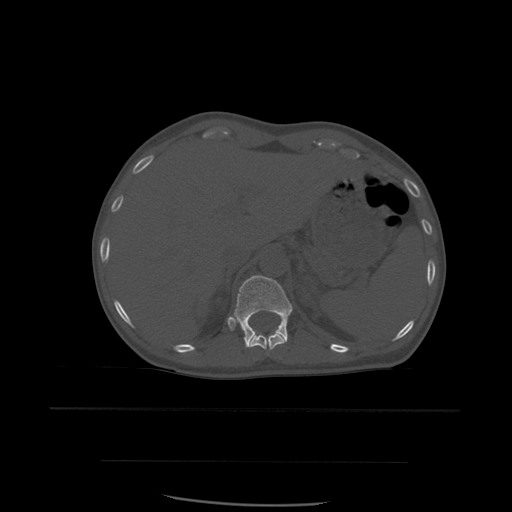
CT including the spine, one axial slice; position 283 of 574 along the scan axis; bone window (W 1800 / L 400 HU); 1.25 mm slice thickness; 512 × 512 image matrix, field of view 392 × 392 mm. Patient age 48 years. From the clinical record (not read from this slice): primary cancer: lung.
Annotated regions visible in this slice (semi-automatic segmentation, software-assisted and operator-edited):
- T11 vertebra: bounding box <250,332,286,350> (left, top, right, bottom; pixels)
- T12 vertebra: <234,276,293,348>